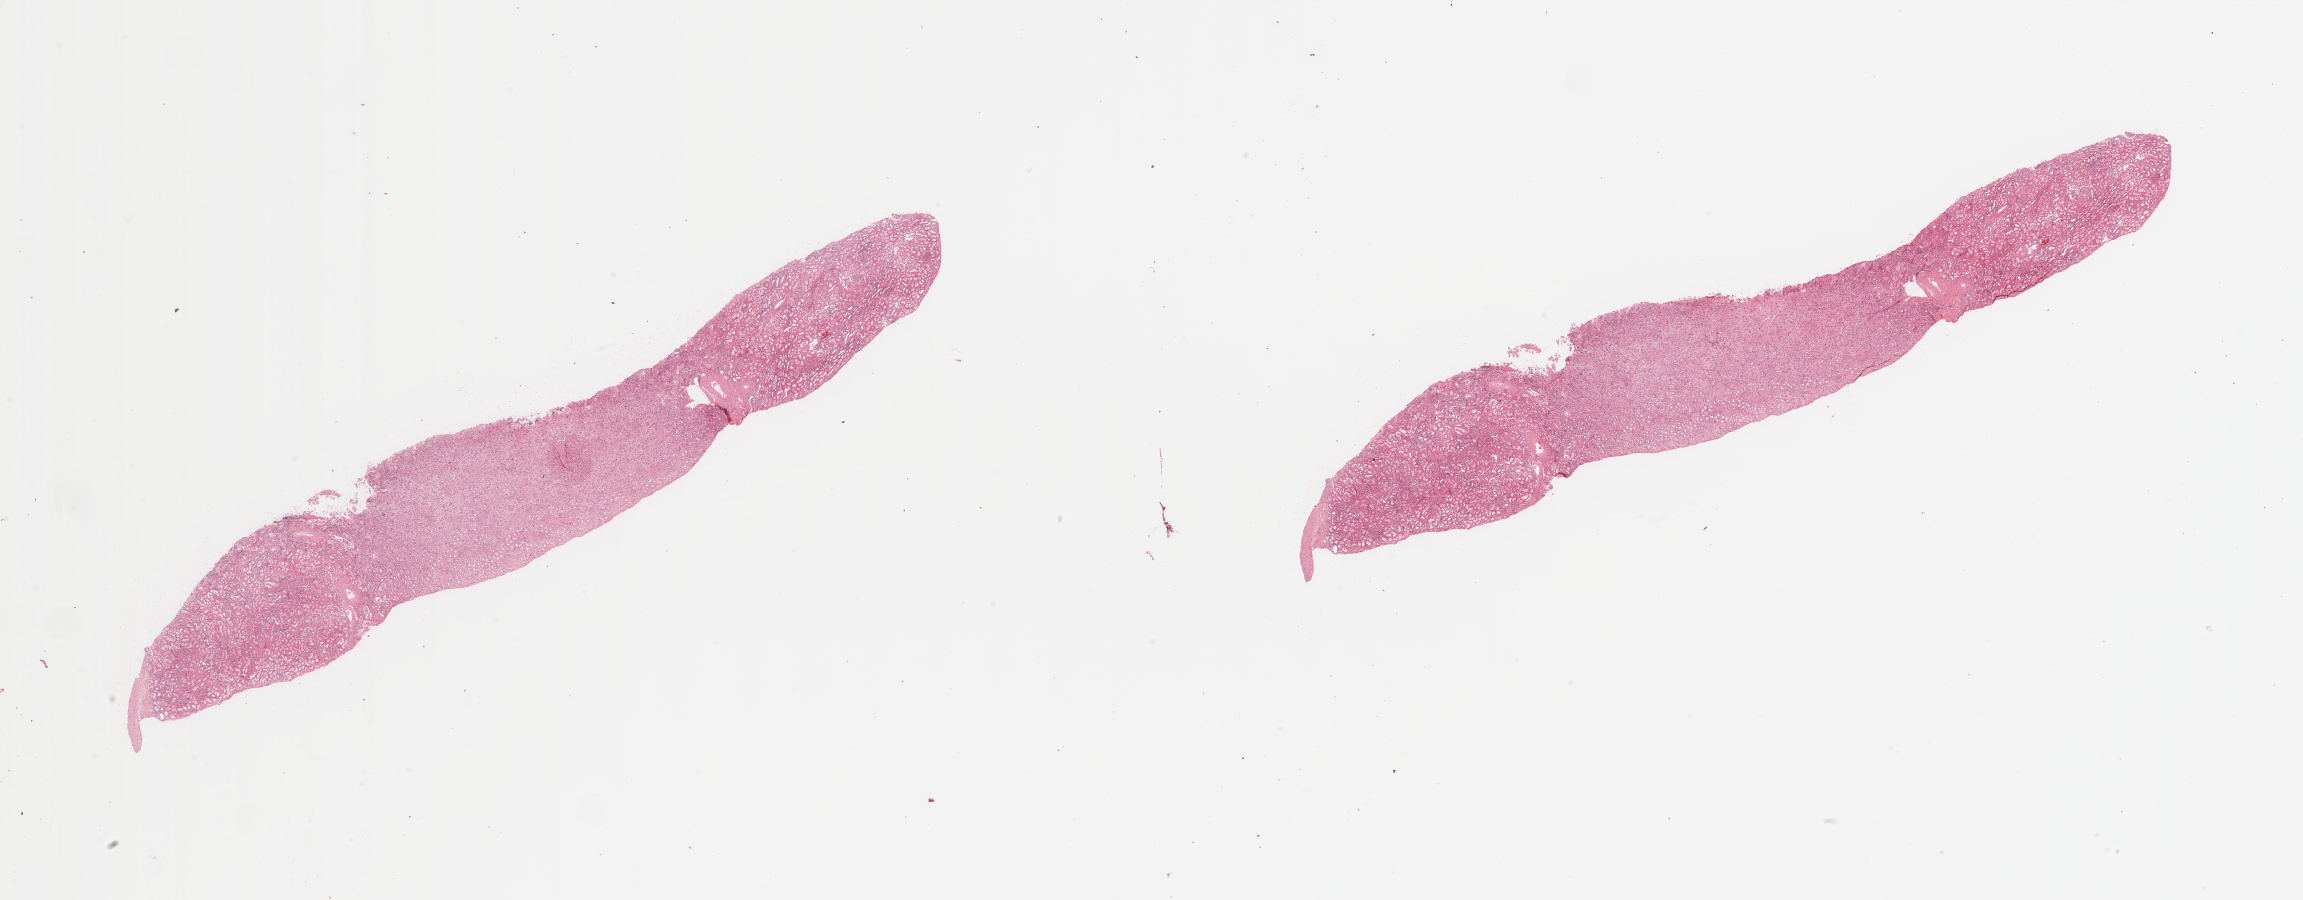
Digitized H&E tissue section (whole slide) — low-resolution overview of the scanned area, about 36.4 x 14.2 mm, normal (non-tumour) tissue sample, sampled site: kidney. 57-year-old male patient.
* this section: normal (non-tumour) tissue from the same patient
* patient diagnosis: Renal cell carcinoma, NOS